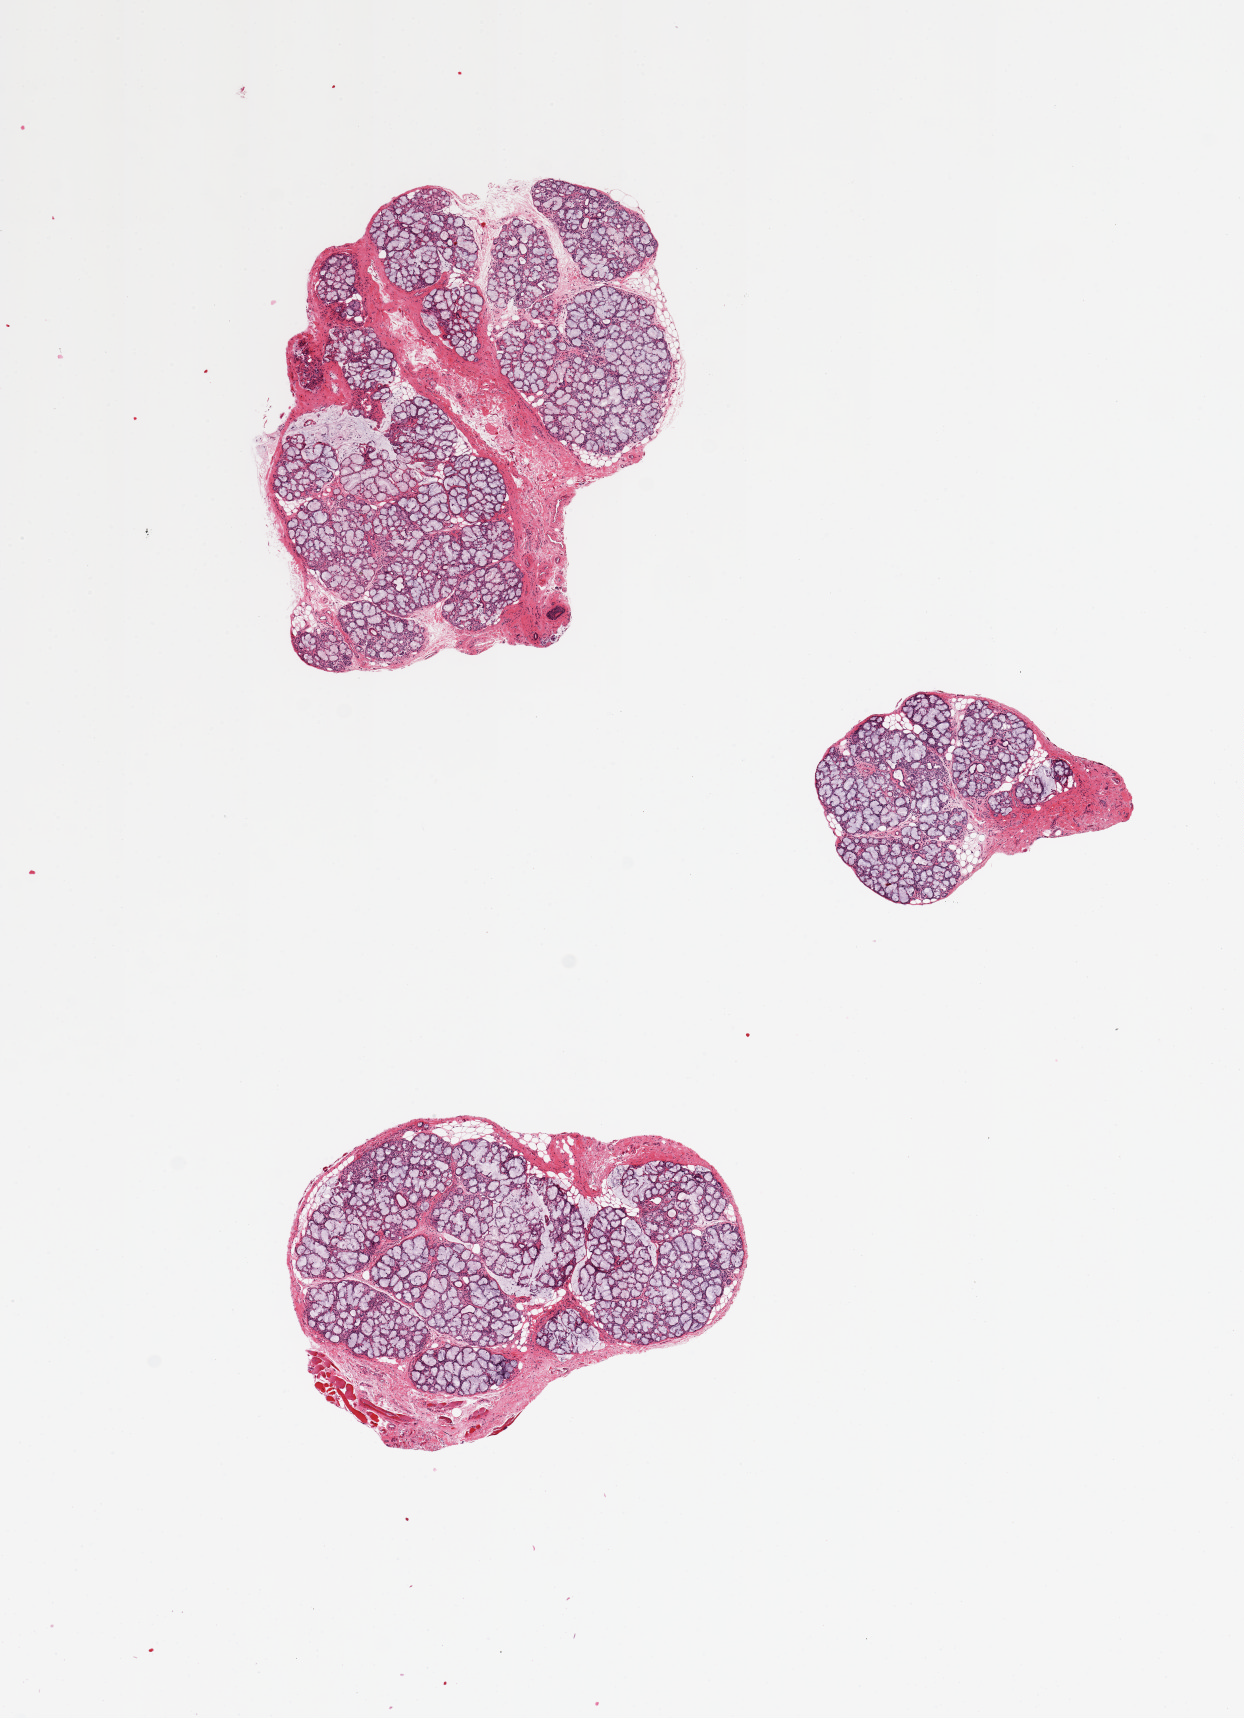
Whole-slide image, H&E stain, a low-resolution overview of the entire scanned area, about 9.8 x 13.6 mm. PAXgene-fixed, paraffin-embedded tissue. Target tissue: minor salivary gland. Donor tissue sample. Donor sex: male.
Review note (as recorded): 3 pieces; excellent dissection.